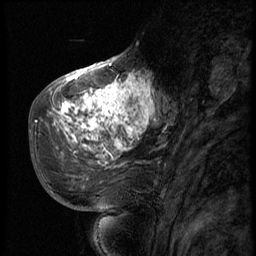
Breast MRI (dynamic contrast-enhanced), one sagittal slice. Slice 26 of 56 in the series (ordered by position). 3 images stored at this slice position (order not interpretable as contrast timing). 1.5 T. TE 4.2 ms, TR 9 ms. 2.5 mm slice thickness. 256 × 256 image matrix, field of view 180 × 180 mm. Patient: female, 51 years. Case-level facts recorded for this patient, not image findings: setting: breast cancer imaged before/during neoadjuvant chemotherapy; receptor status: triple-negative.
Outlined on this slice (semi-automatic segmentation, software-assisted and operator-edited):
- analysis volume of interest (the breast-tissue region the enhancement analysis was run in; not a lesion): box from (x=52, y=66) to (x=161, y=179) px
- tumour enhancement mask (voxels above the 140 % enhancement threshold inside the analysis volume of interest): (x=52, y=74)–(x=155, y=157)